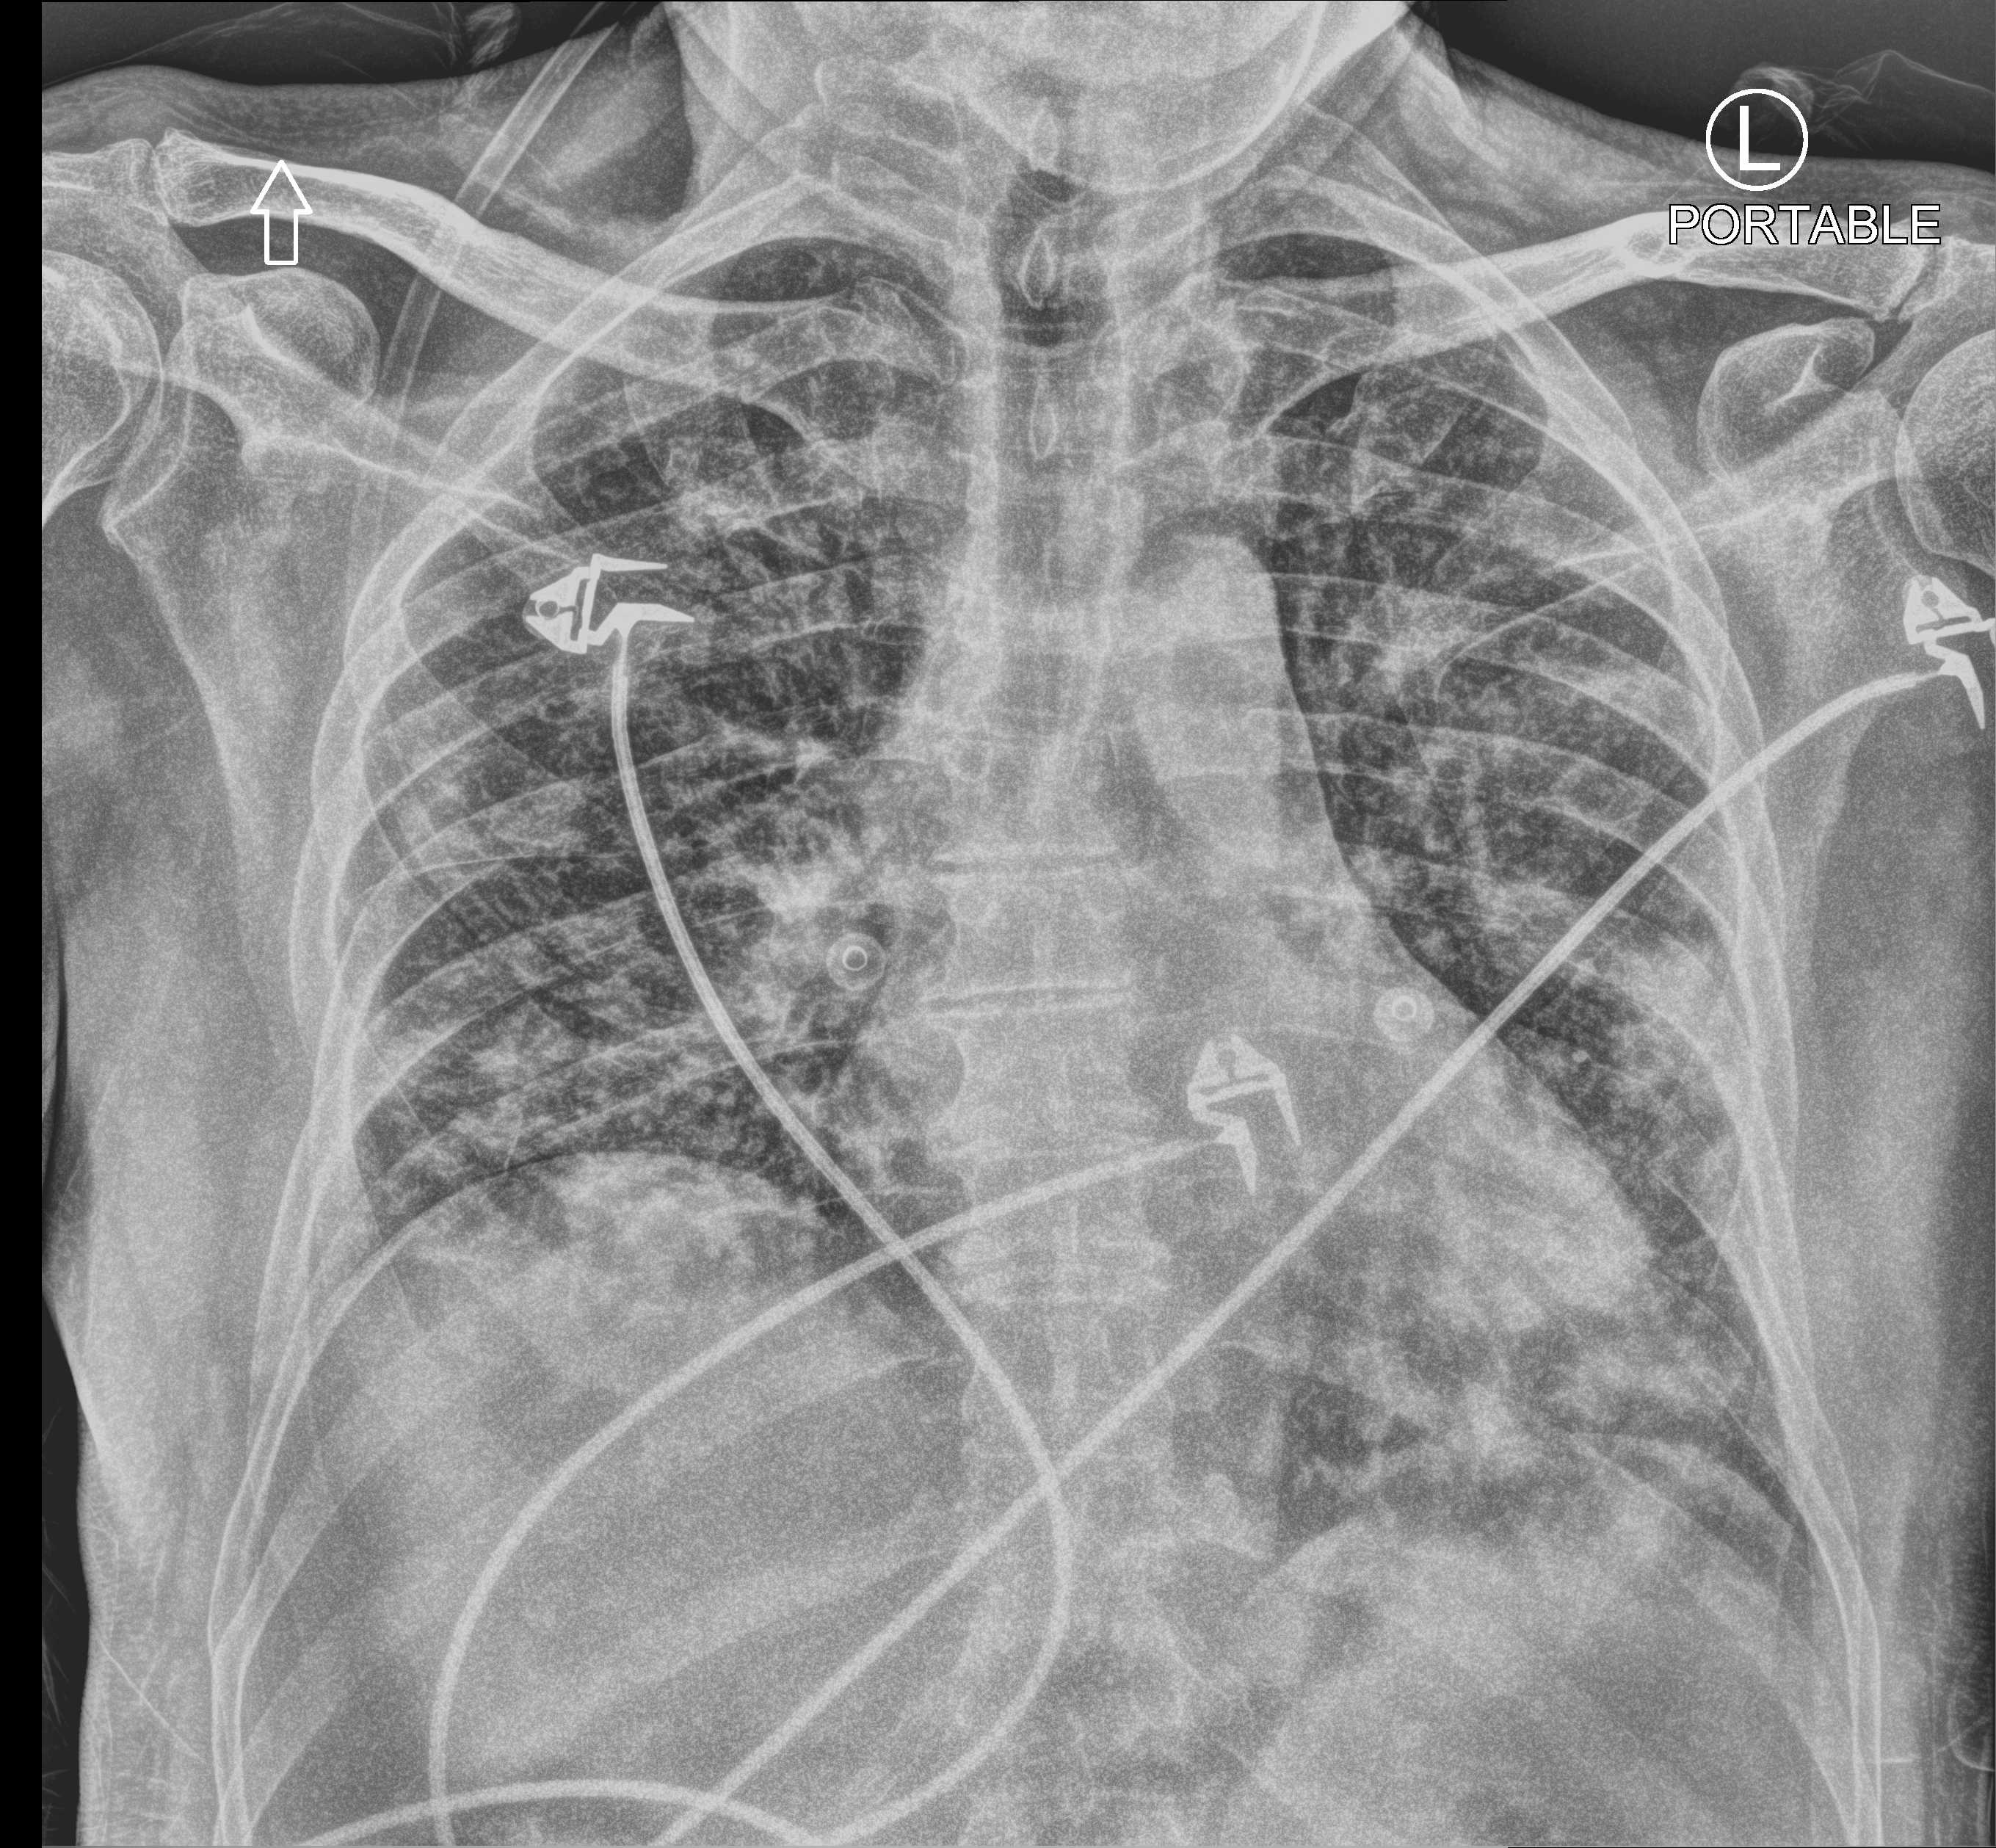
Portable chest radiograph, anteroposterior (AP) projection. Patient hospitalised with COVID-19; male, aged 60–74 years.
Hospital-stay facts (about this admission, not read from this image; timing relative to this image not recorded):
- length of hospital stay: 12 days
- admitted to intensive care during this hospital stay: no